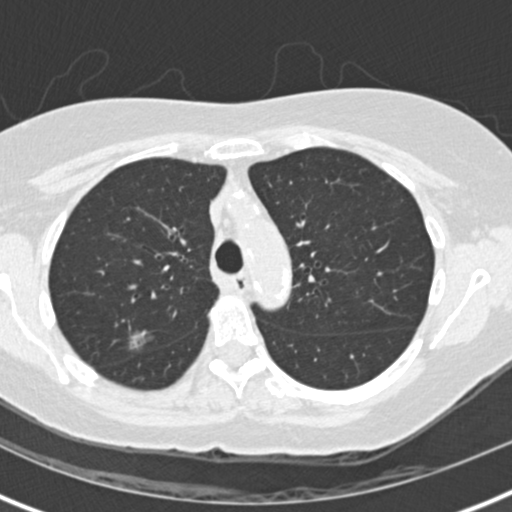
Axial slice from a low-dose chest CT screening exam; baseline annual screen; lung window (W 1500 / L -600 HU); 2 mm slice thickness; 120 kVp; slice 46 of 147 in the series. Female, age 72 years at enrolment. Current smoker at enrolment.
Expert-annotated lung lesion, box from (x=108, y=316) to (x=168, y=369) px. Reader record for this screening exam (exam-level; its link to the box is not recorded): non-calcified nodule or mass ≥4 mm, right upper lobe, 11 × 11 mm, poorly defined margins, ground glass attenuation. Participant outcome: lung cancer diagnosed 75 days after this screen — bronchiolo-alveolar adenocarcinoma, NOS, right upper lobe, well differentiated (G1), stage IA (AJCC 6th edition), 23 mm at pathology.